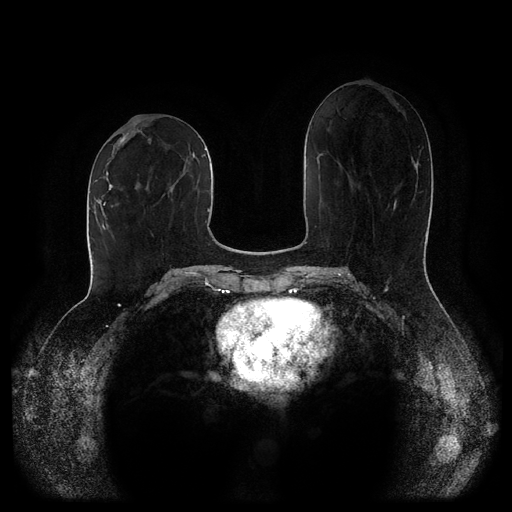
Breast MRI (dynamic contrast-enhanced, multi-phase), one axial slice; position 45 of 116 along the scan axis; dynamic contrast-enhanced series, time point 2 of 5 at this slice position (early post-contrast); 1.5 T; TE 2.6 ms, TR 5.2 ms; 512 × 512 image matrix, field of view 380 × 380 mm. Patient: female, 52 years.
Structures marked on this image (semi-automatically segmented with operator editing):
- breast lesion (labelled 'tumour' in the annotation; benign lesions carry a separate 'benign' label): box from (x=120, y=132) to (x=133, y=144) px